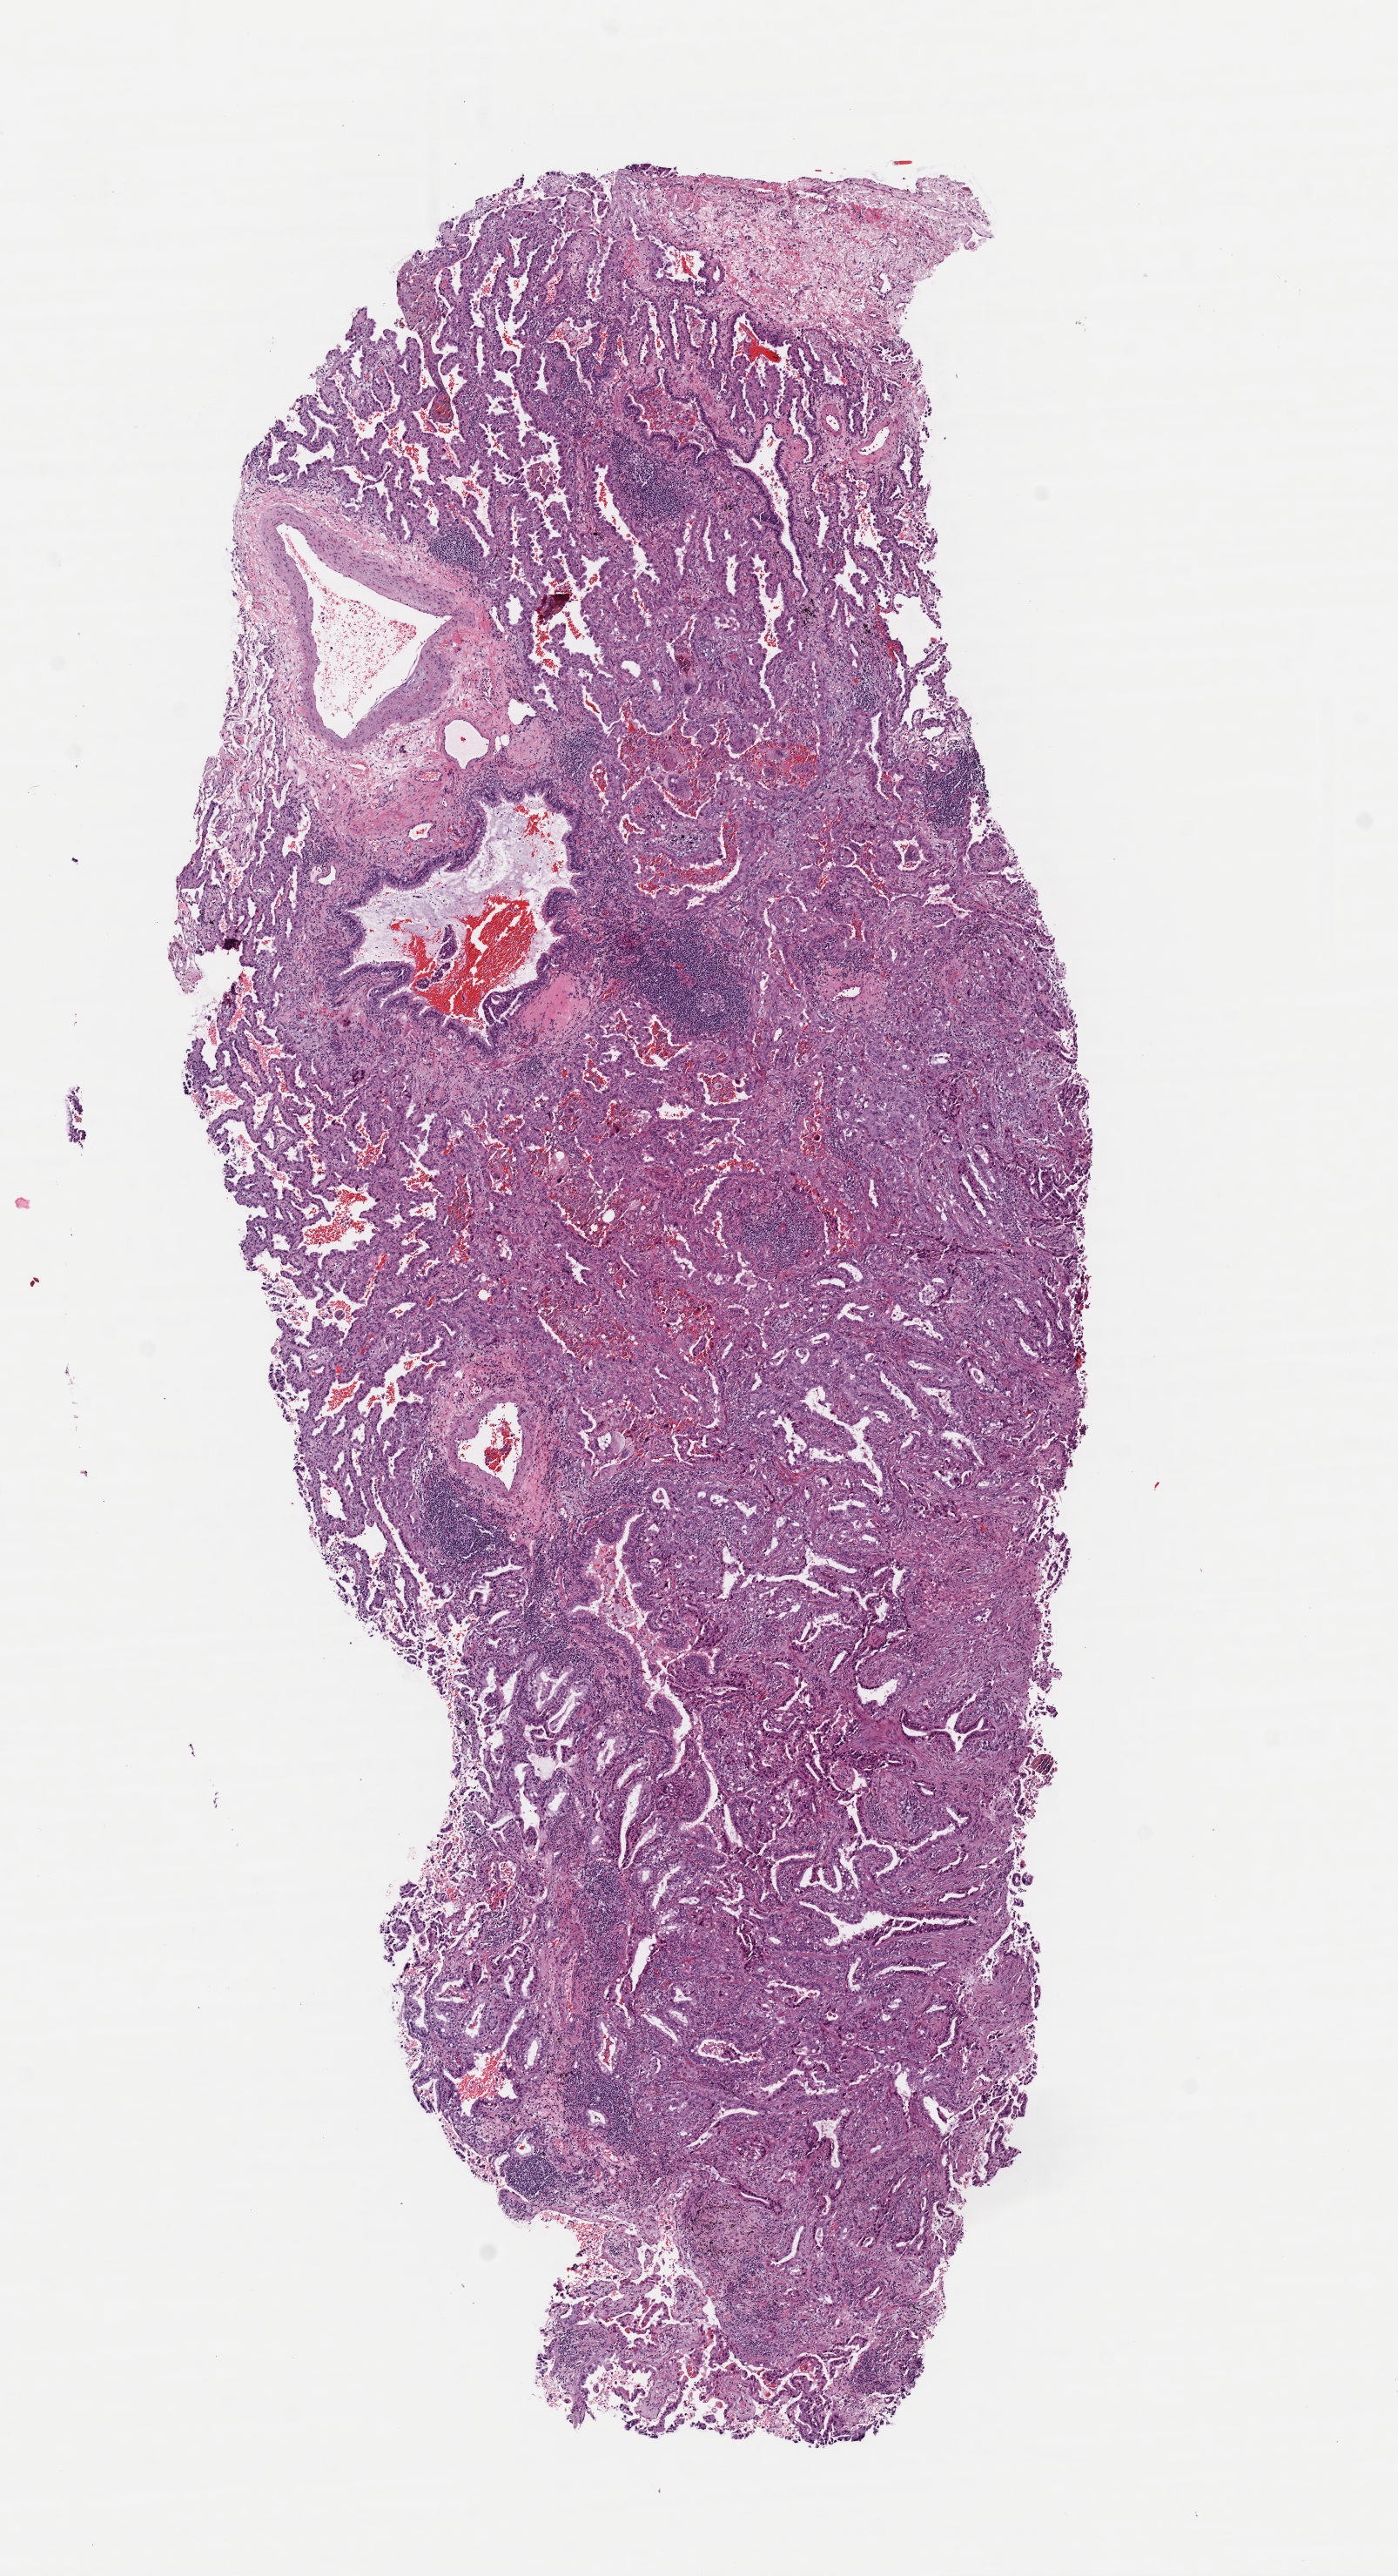
Whole-slide histology image, Hematoxylin and eosin (H&E) stained — shown as a low-resolution overview of the whole scanned area (about 6.3 x 11.7 mm, from a 40x scan); frozen section; lung, primary tumour sample. Patient: female, age at initial diagnosis 72 years. Slide review estimates, as recorded: tumour cells 80%, tumour nuclei 80%, normal cells 5%, stromal cells 15%, necrosis 0%. Inflammatory infiltration, as recorded: lymphocyte infiltration 20%, monocyte infiltration 8%, neutrophil infiltration 0%.
* laterality: right
* histologic diagnosis: Adenocarcinoma, NOS (upper lobe, lung)
* TNM: T2a N0 MX
* AJCC pathologic stage: IB (7th edition)